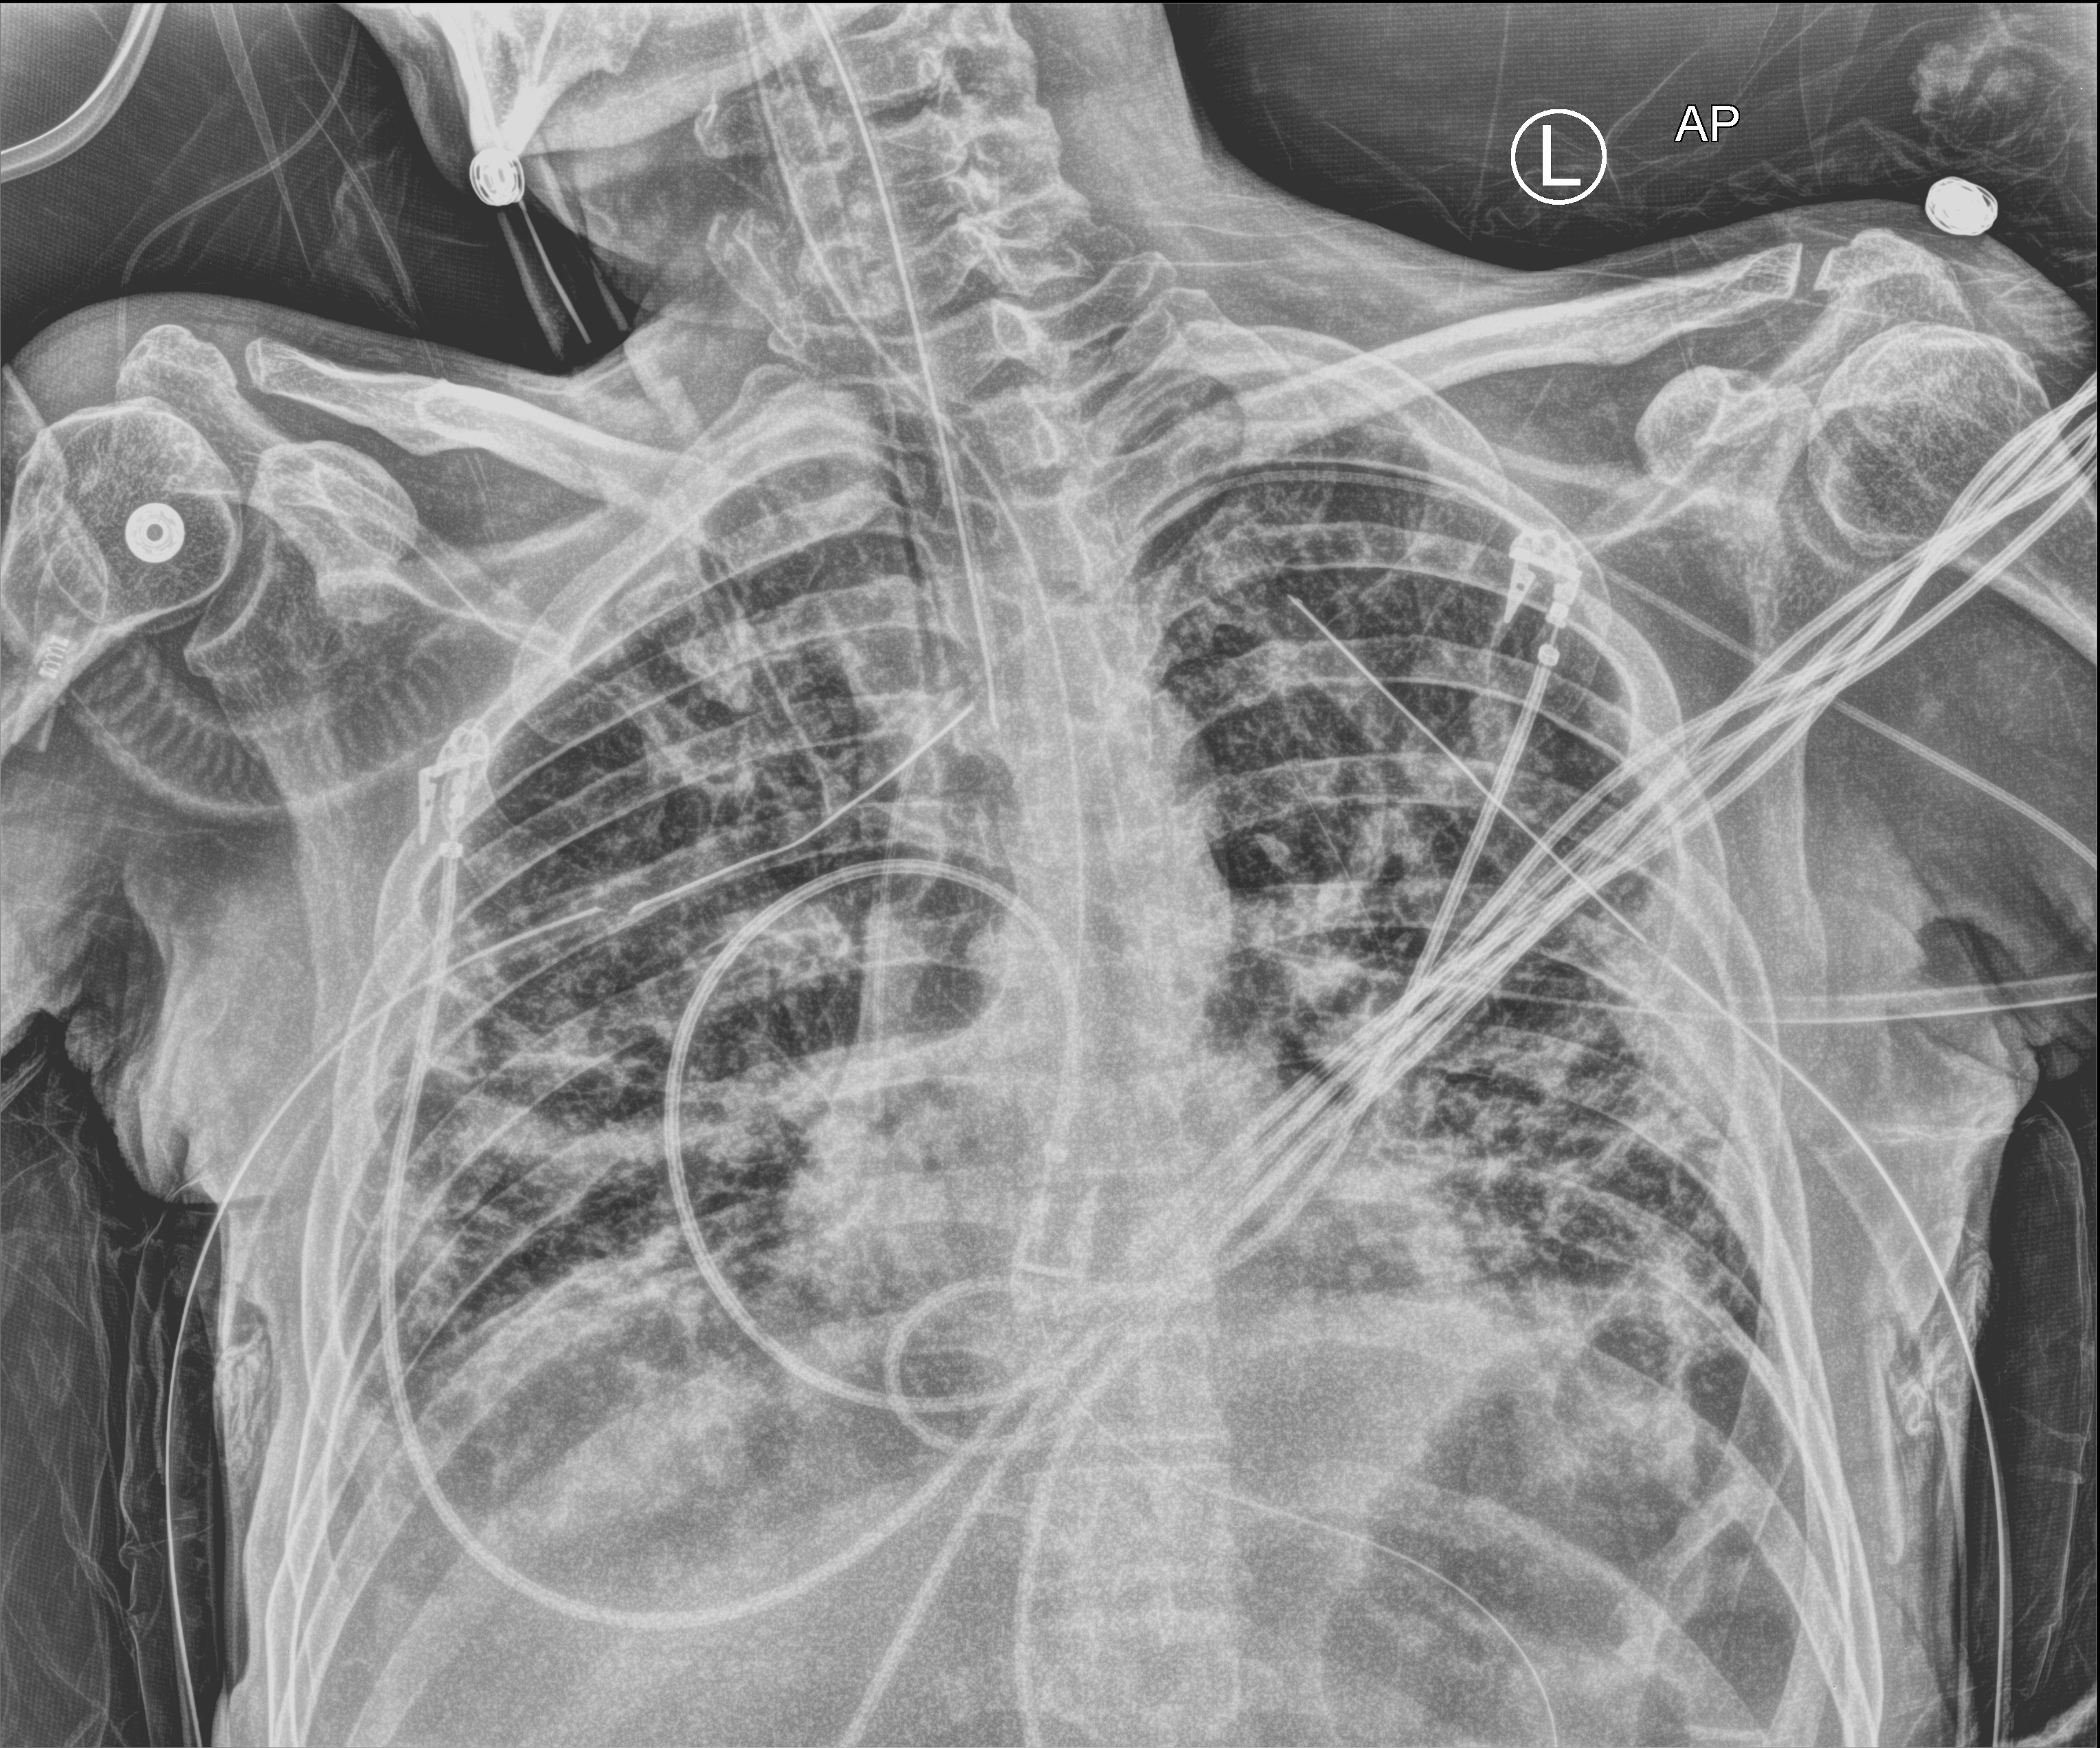
Bedside chest radiograph (computed radiography); anteroposterior (AP) projection. Male patient hospitalised with COVID-19, age 18–59 years.
From the hospital-stay record, not from the radiograph (when in the stay this image was taken is not recorded):
- admitted to intensive care during this hospital stay: yes